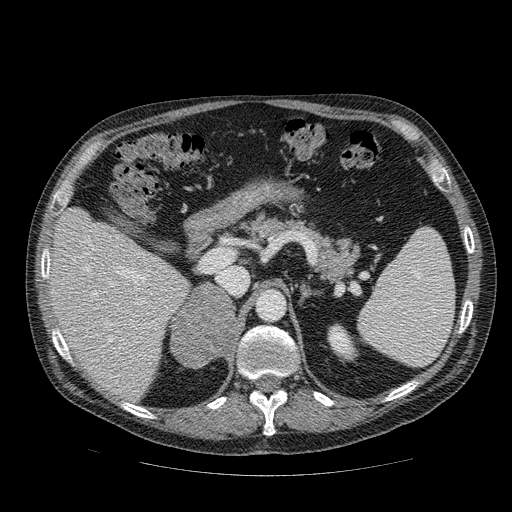
Contrast-enhanced abdominal CT, one axial slice; position 58 of 111 along the scan axis; reconstruction kernel STANDARD; intravenous contrast given; soft-tissue window (W 400 / L 40 HU); 512 × 512 image matrix. Male patient, age 56 years. Case-level facts recorded for this patient, not image findings: diagnosis: adrenocortical carcinoma; tumour side: right adrenal; tumour size at pathology: 9 cm; Ki-67 index: 48 %; stage (as recorded): 4.
Outlined on this slice (semi-automatic segmentation, software-assisted and operator-edited):
- mass: box from (x=171, y=284) to (x=235, y=367) px